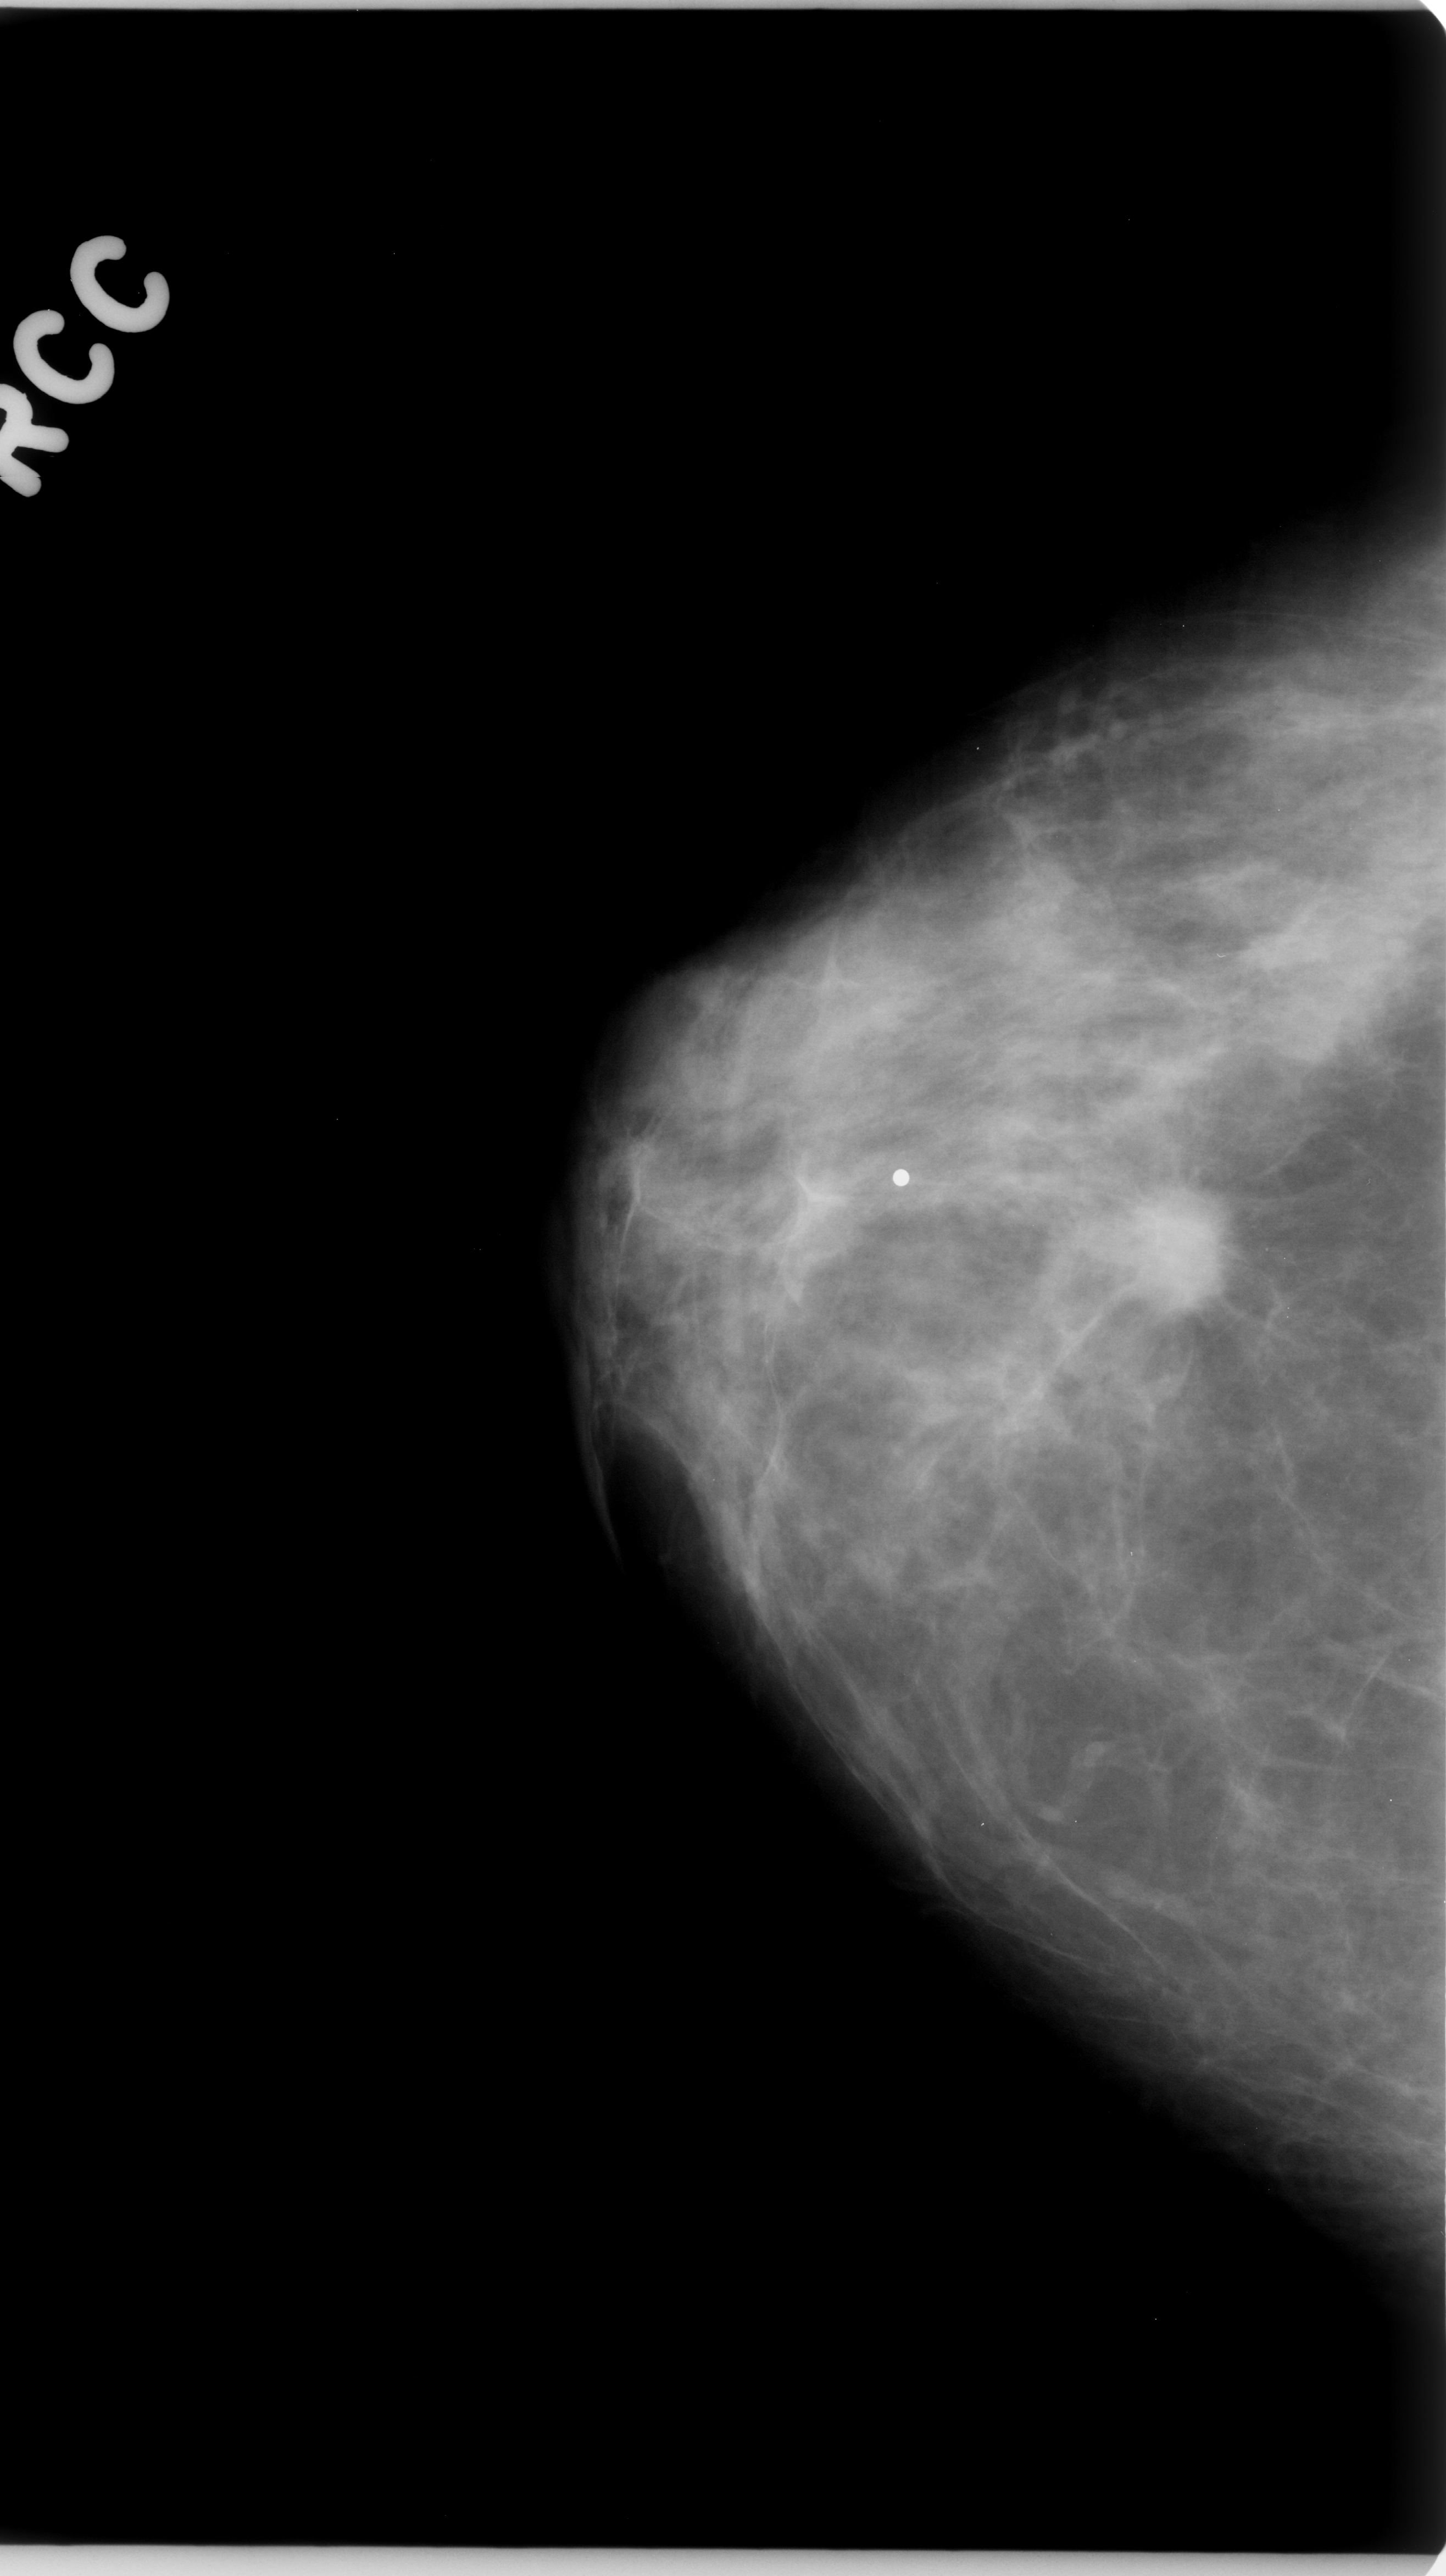
Digitized screen-film mammogram, right breast, CC view, BI-RADS breast density category 2 (scale 1–4).
Marked abnormality: mass, shape irregular, margins spiculated; BI-RADS assessment category 5; subtlety rating 5 on a 1 (subtle) to 5 (obvious) scale; pathology result (as recorded, not read from the image): malignant.